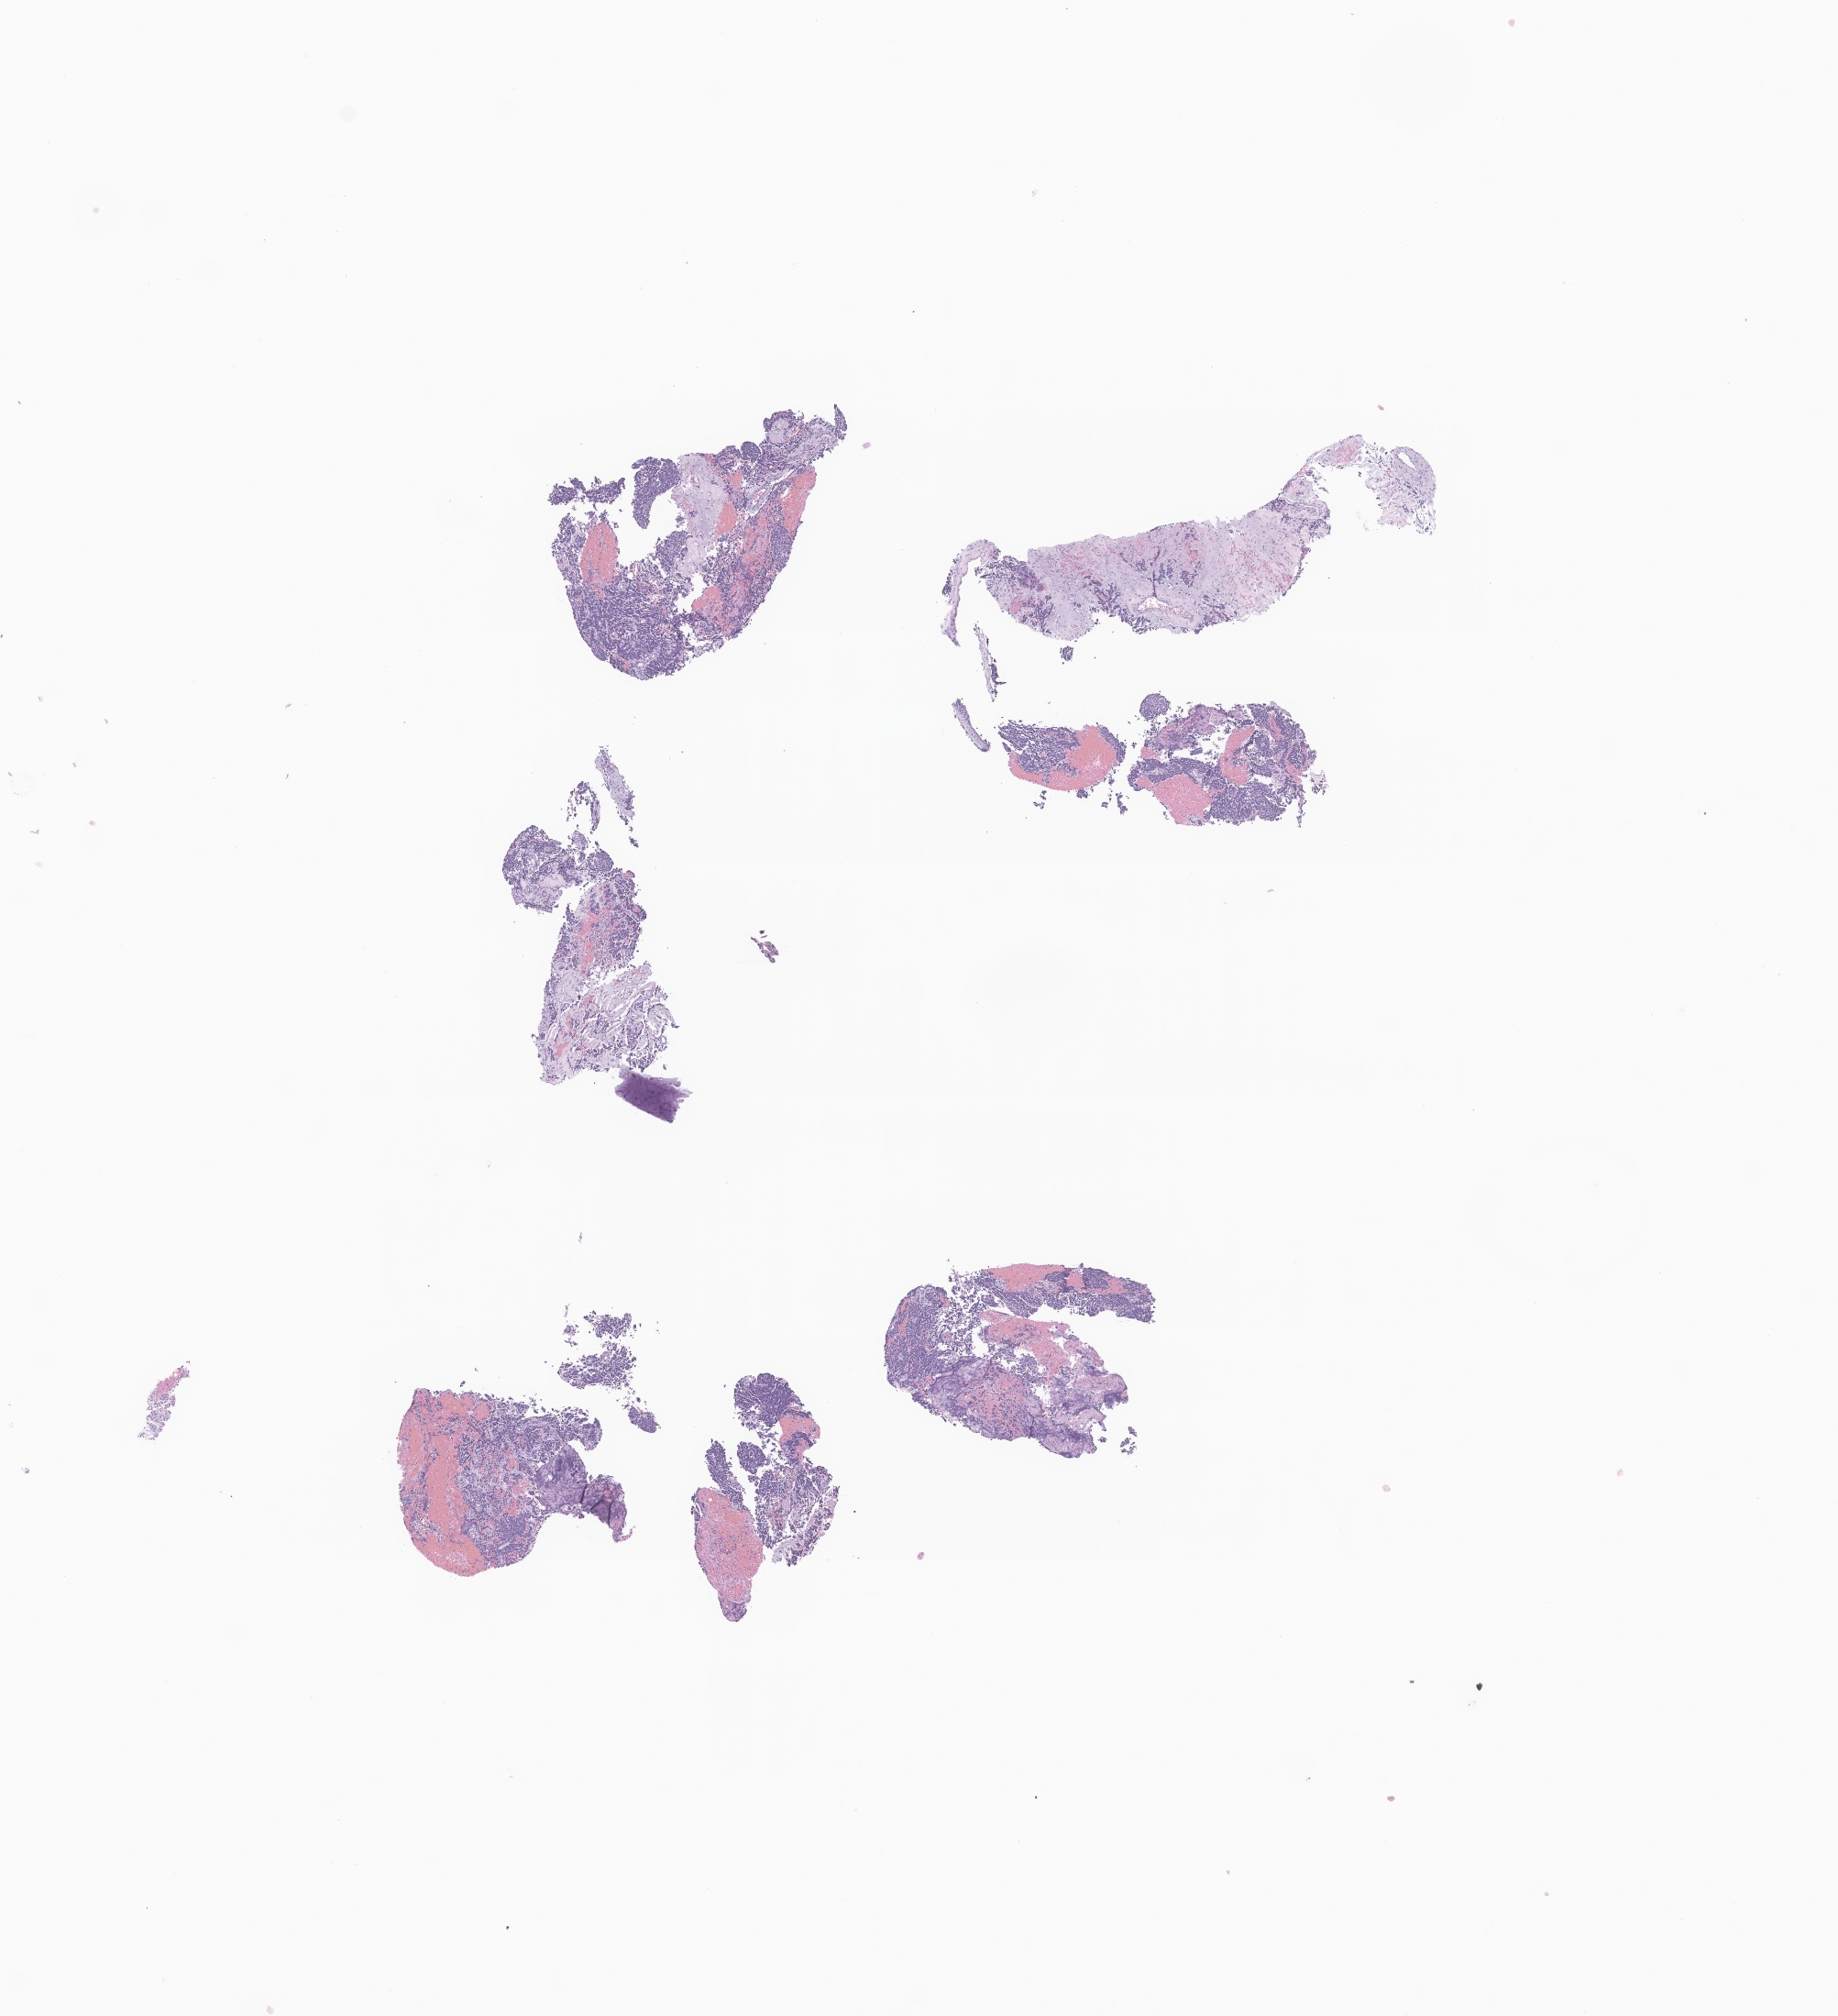
Whole-slide image, haematoxylin and eosin stain of tumor tissue from the adrenal gland, shown as a low-resolution overview of the whole scanned area (about 8.5 x 9.3 mm). Formalin-fixed paraffin-embedded section. Female patient, age 415 days (about 1.1 years).
Diagnosis (ICD-O-3 morphology term): Neuroblastoma, NOS.